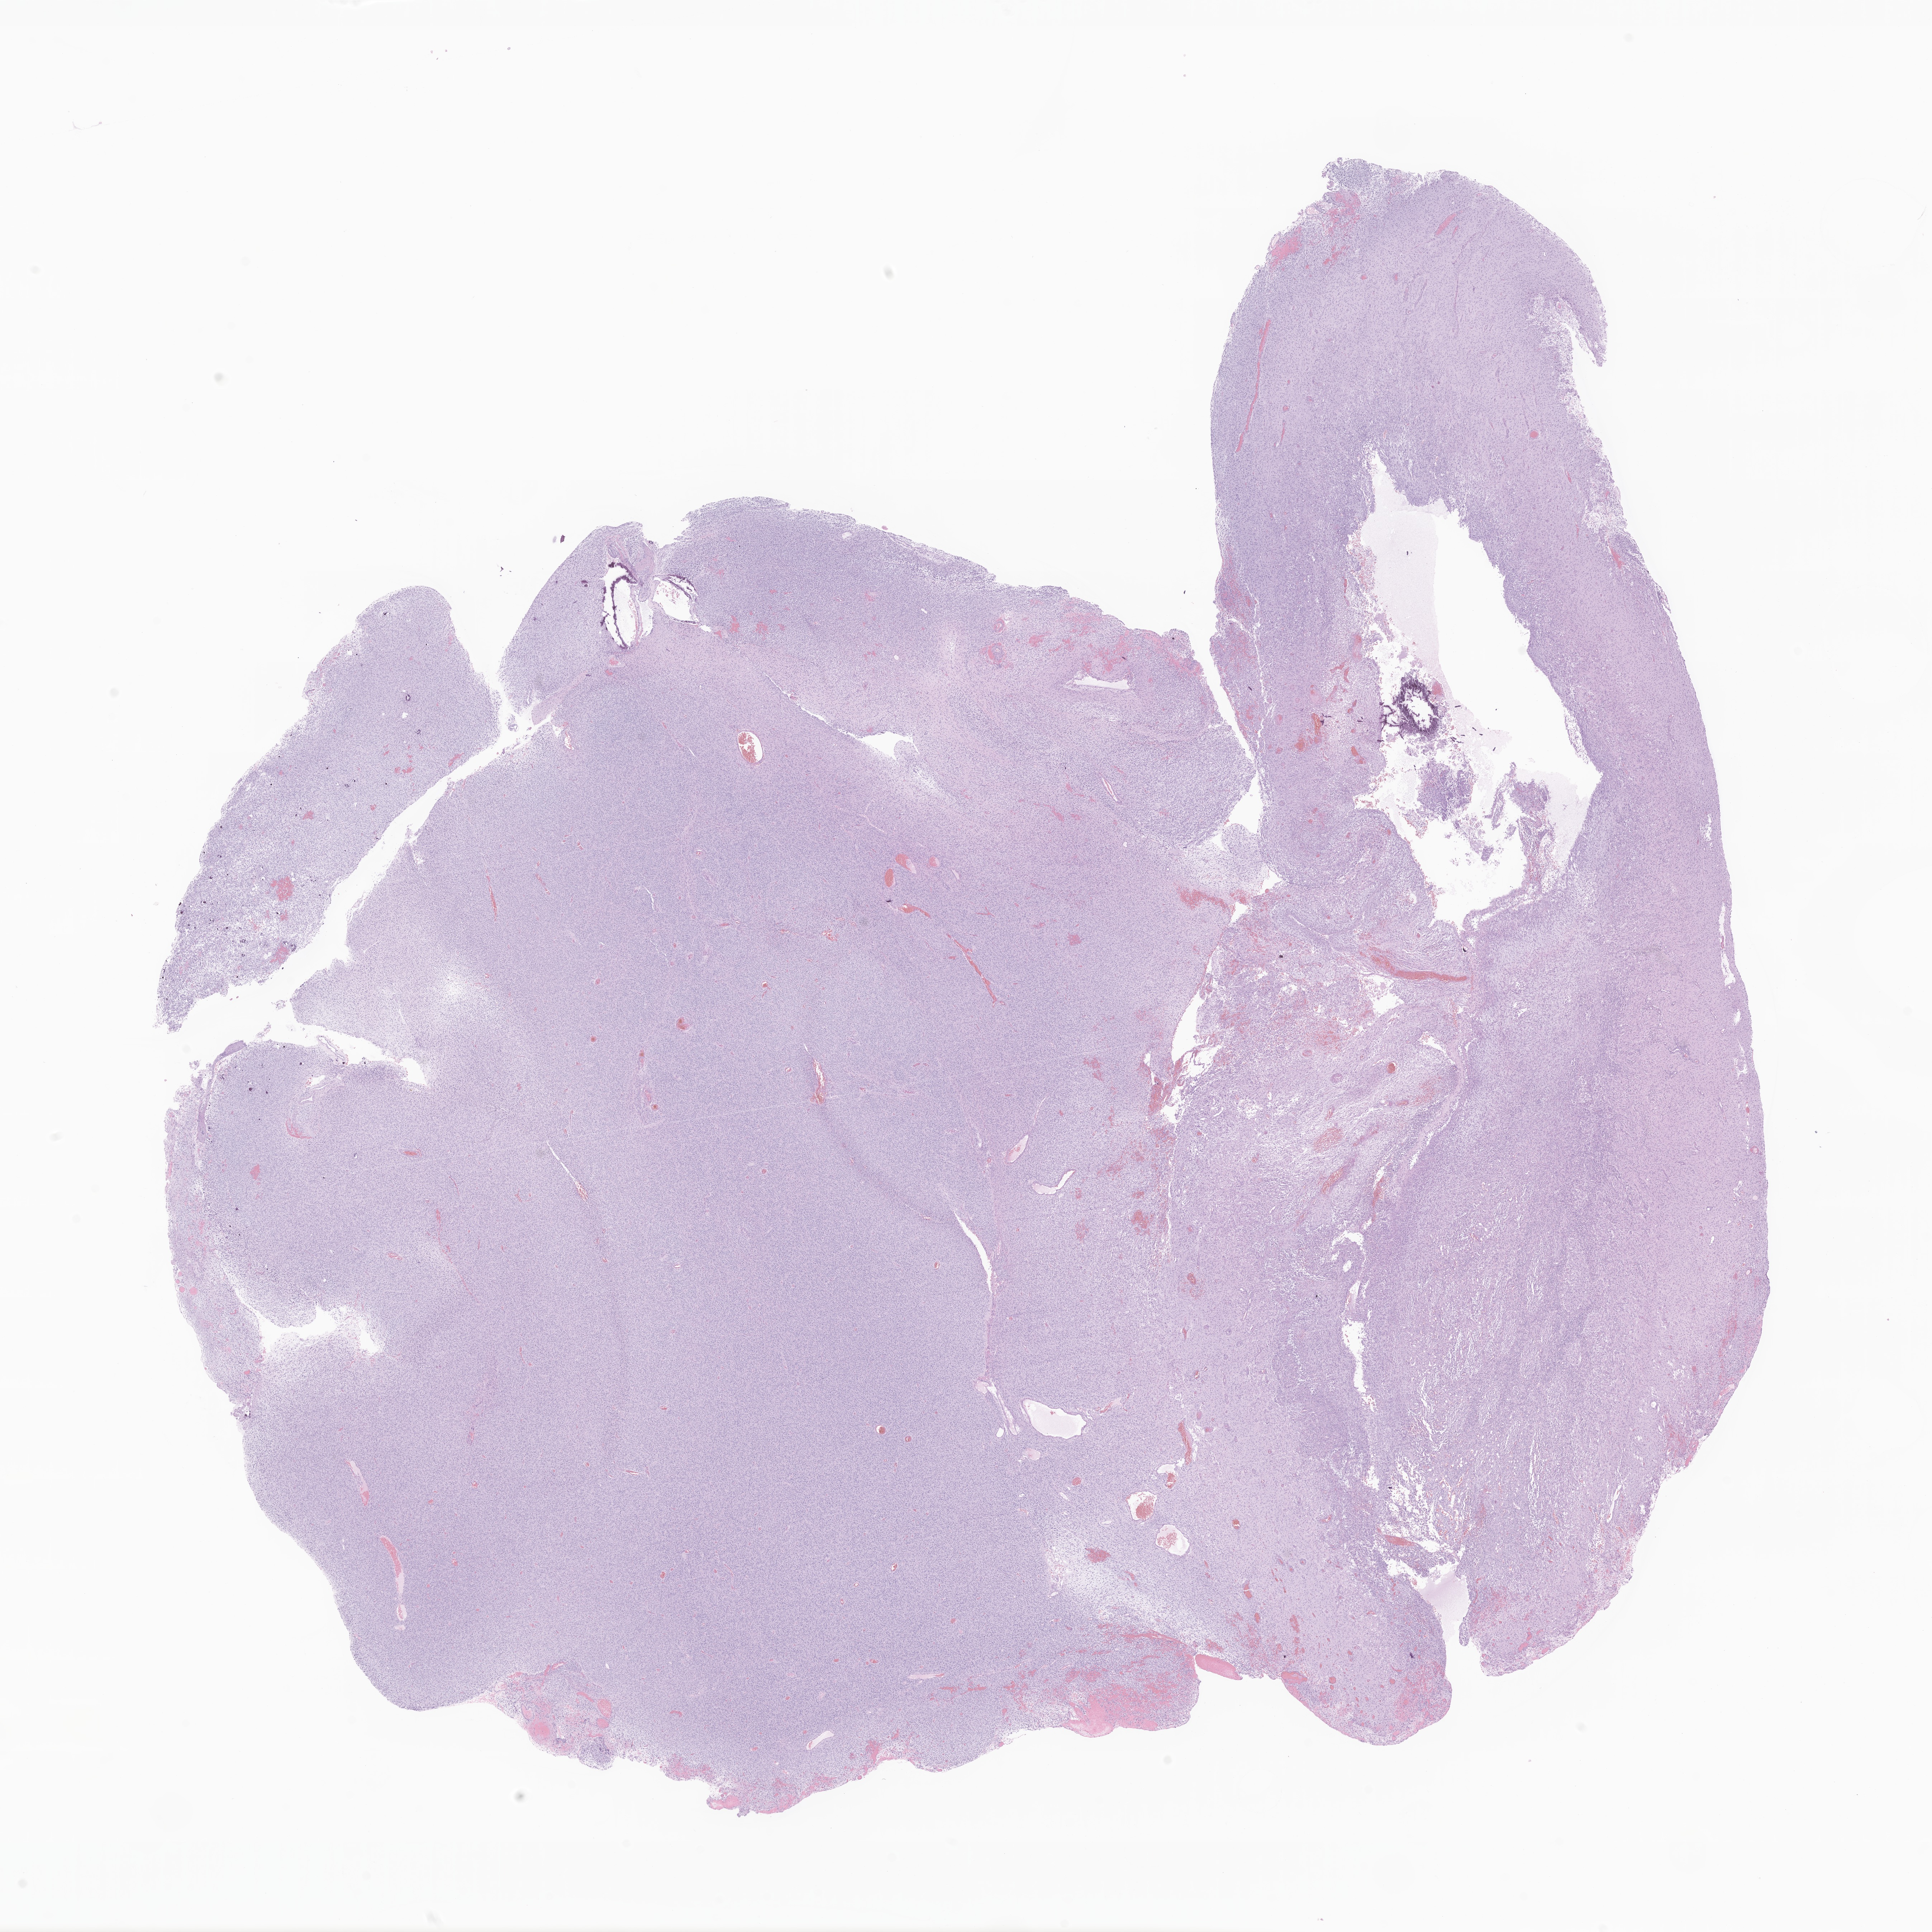
Digitized haematoxylin and eosin-stained section of tumor tissue from the brain, shown as a low-resolution overview of the whole scanned area (about 22.7 x 22.7 mm); formalin-fixed, paraffin-embedded (FFPE) tissue. Female patient, age 80 months (6 years 8 months).
Recorded diagnosis: Neoplasm, uncertain whether benign or malignant.